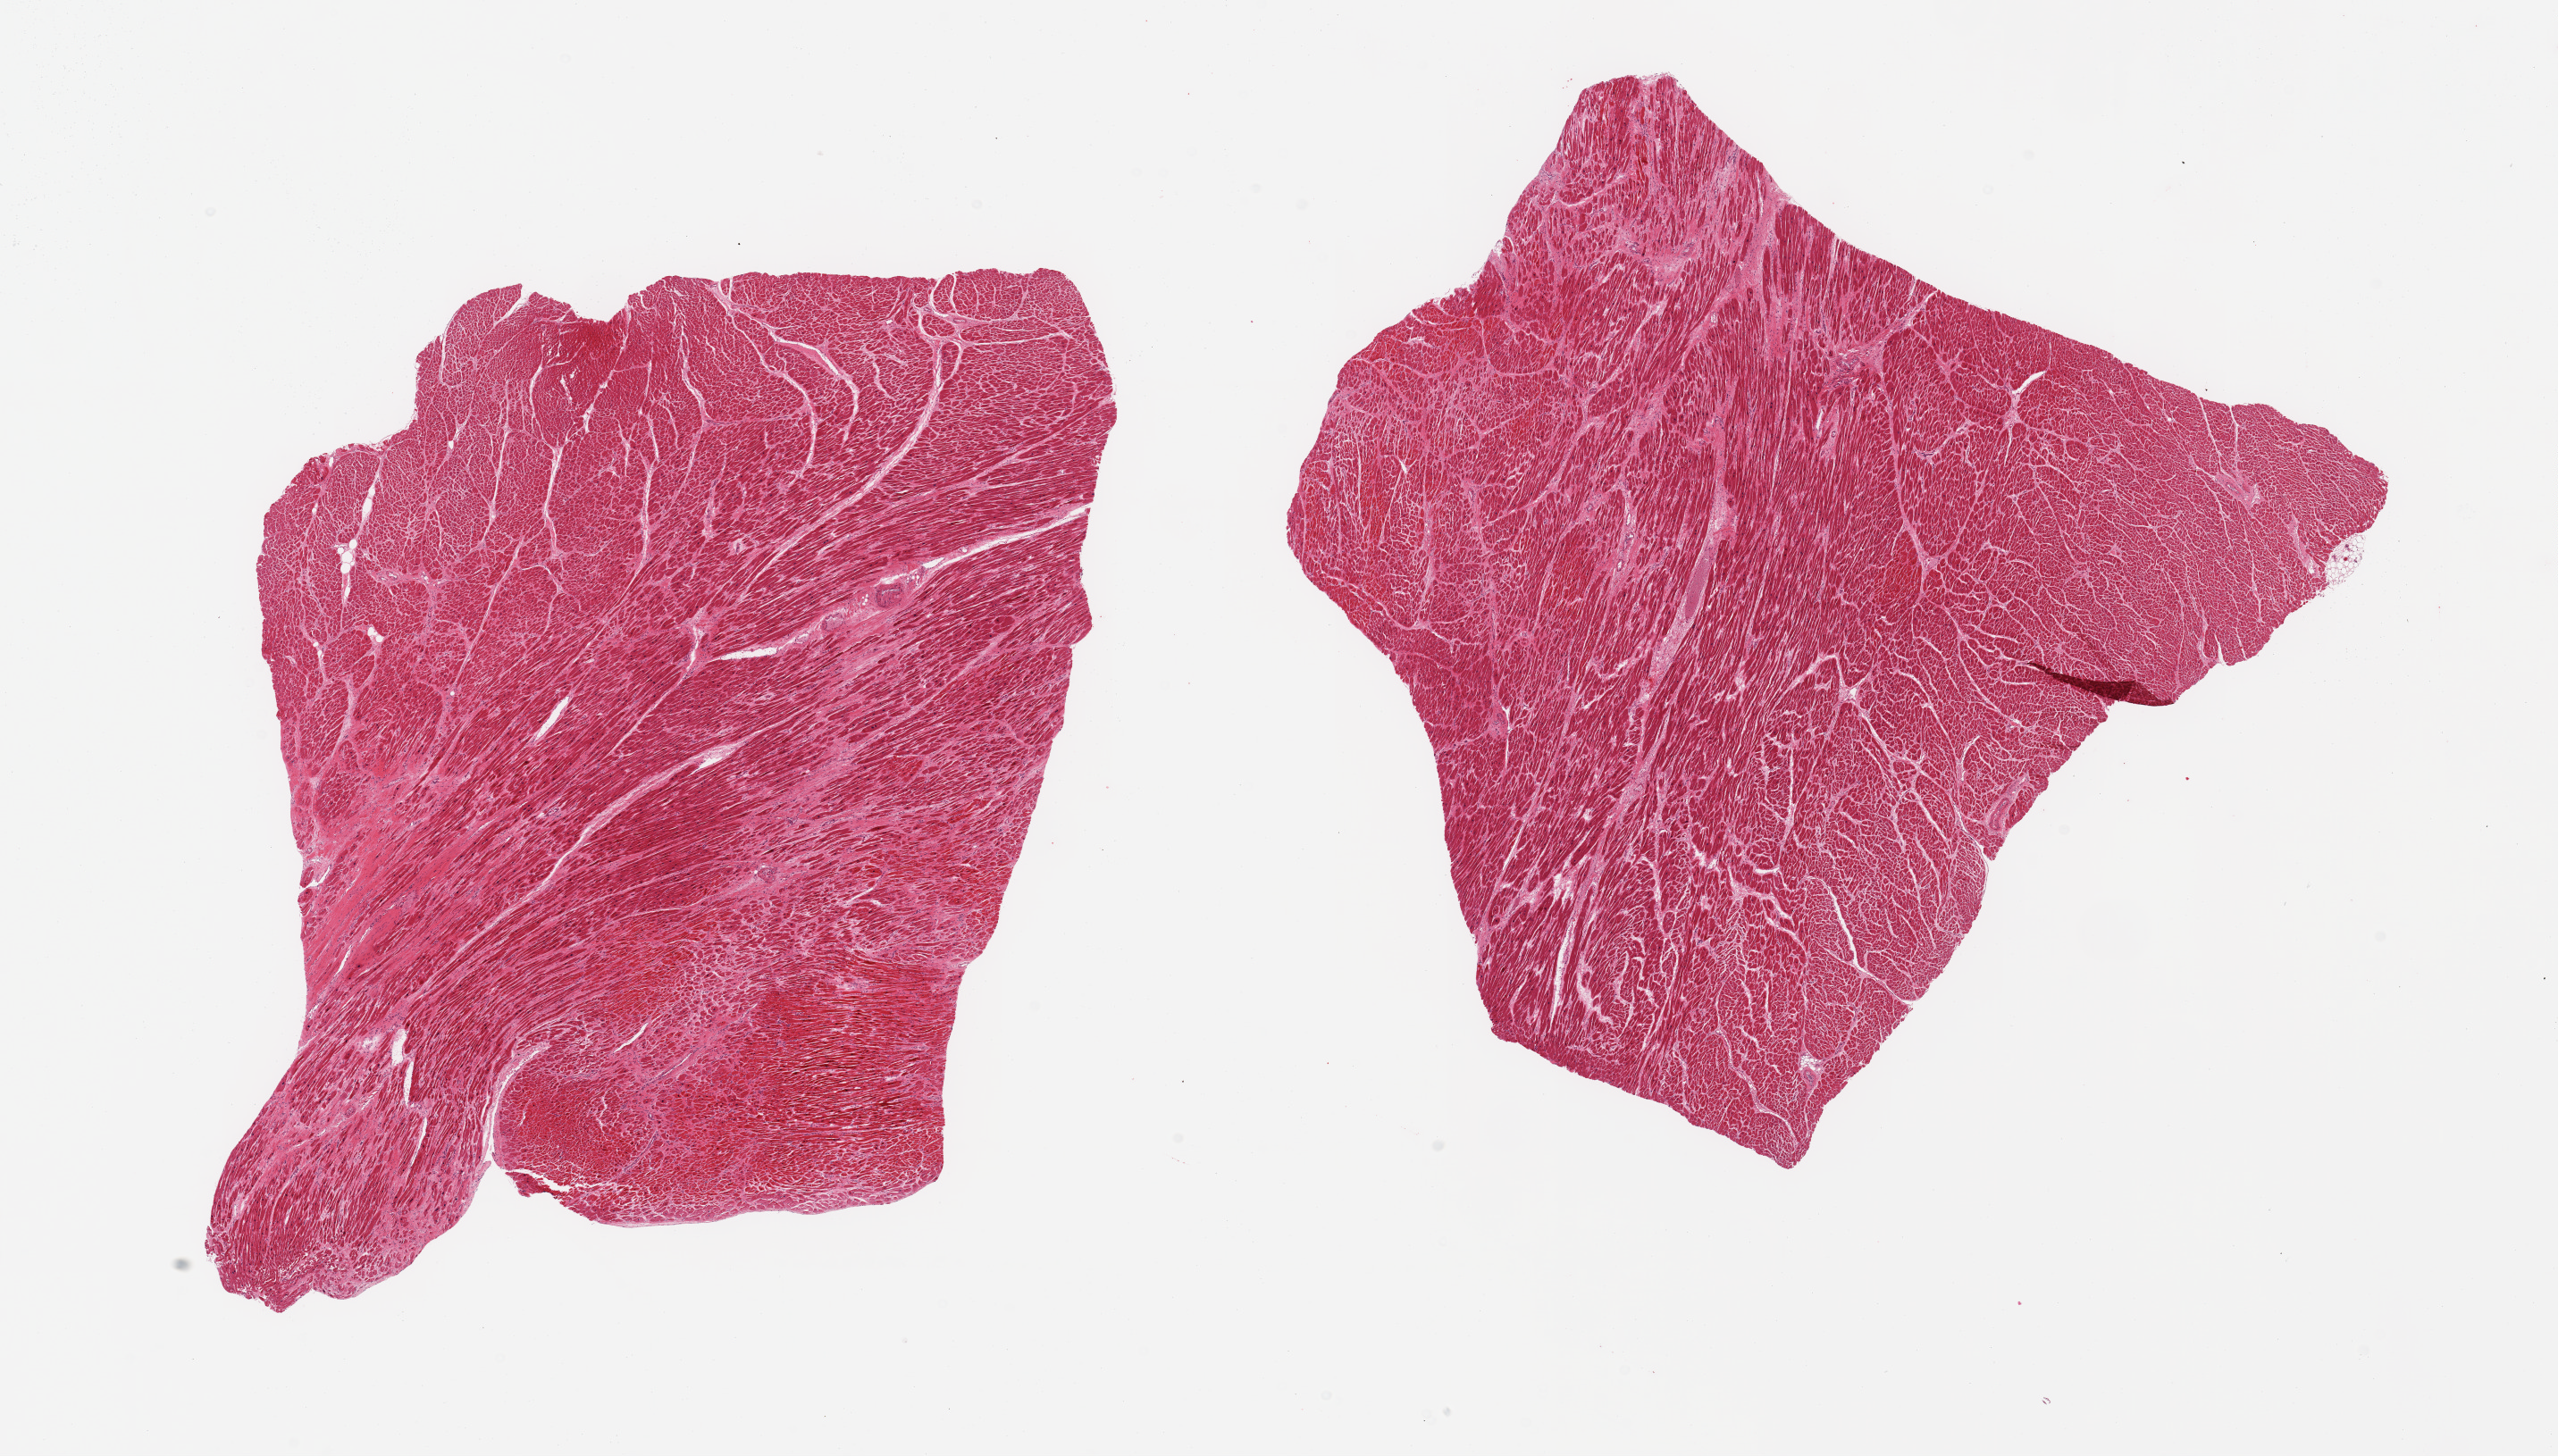
Digitized hematoxylin and eosin (H&E)-stained section, brightfield, low-resolution overview of the scanned area, about 22.6 x 12.9 mm. PAXgene-fixed paraffin-embedded (PFPE) section. Target tissue: heart. Tissue donor sample. Donor sex: male.
Review note (as recorded): 2 pieces multifocal remote infarcts up to ~5mm, patchy interstitial fibrosis.